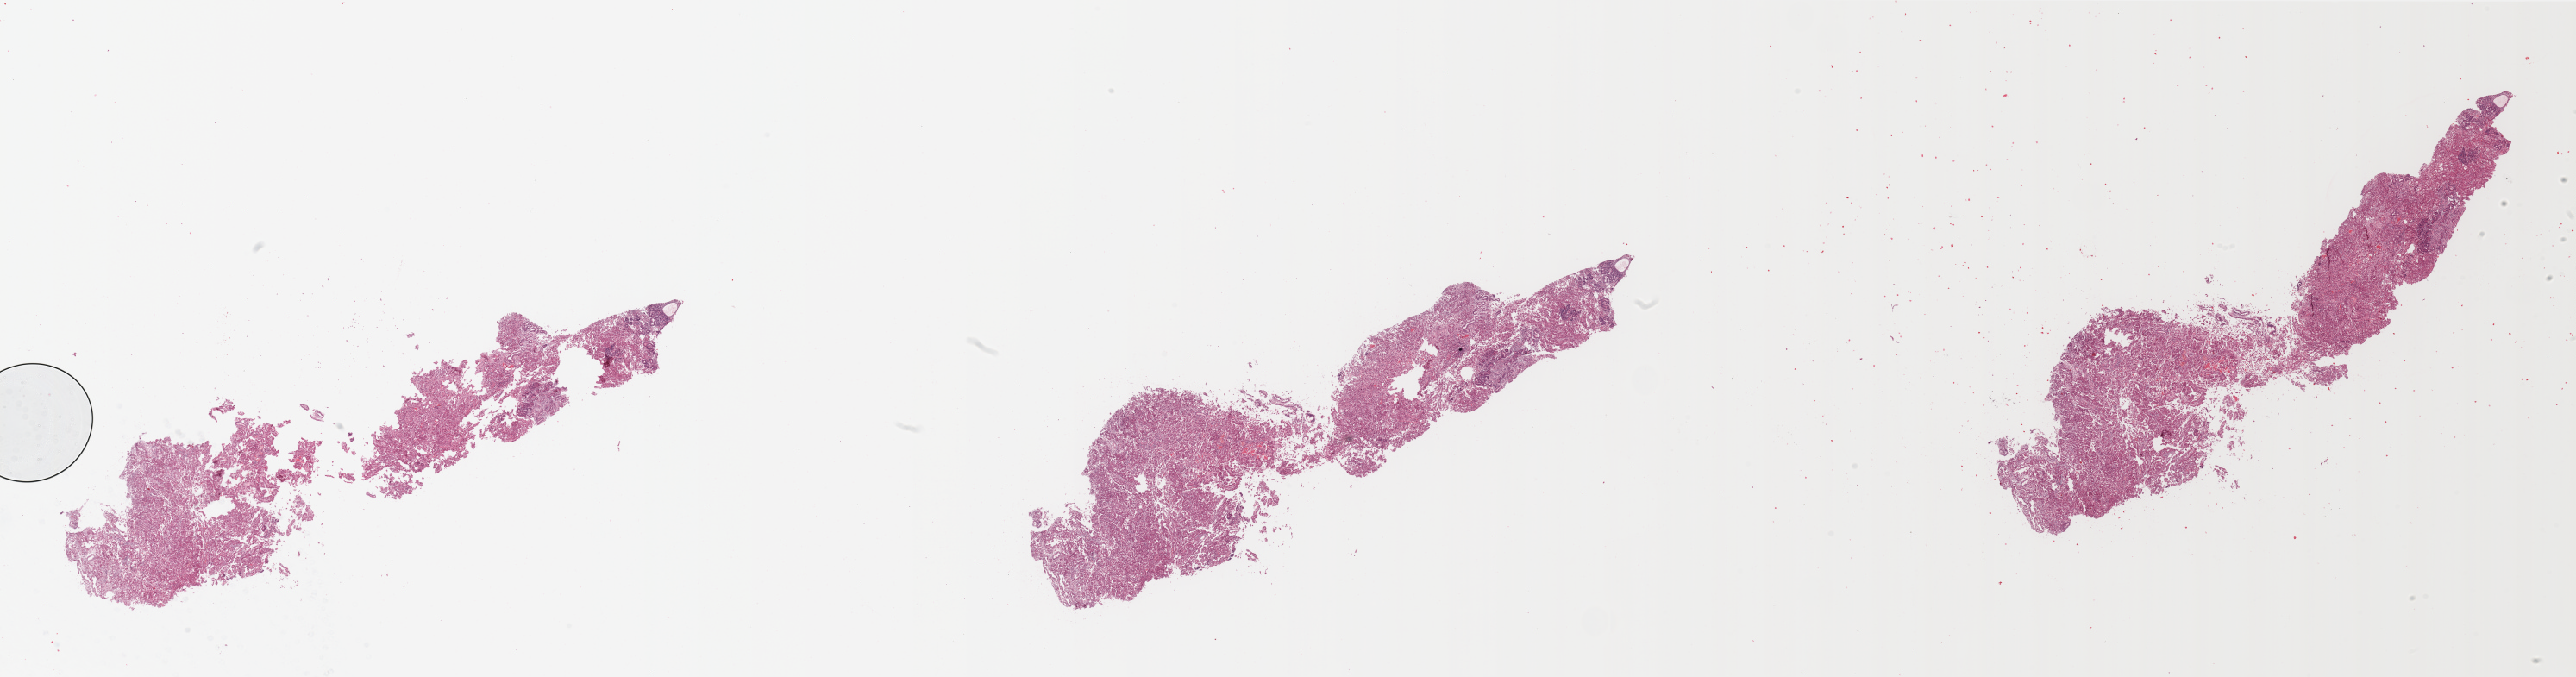
Whole-slide histology image, H&E-stained, whole scanned area (about 47.3 x 12.4 mm, slide scanned at 20x) shown as a low-resolution overview. Tumour tissue sample, sampled site: uterus. 72-year-old female patient. Histologic grade: G3 (poorly differentiated). Slide review estimates, as recorded: tumour nuclei 90%, necrosis 5%.
- diagnosis: Endometrioid adenocarcinoma, NOS
- AJCC pathologic stage: III